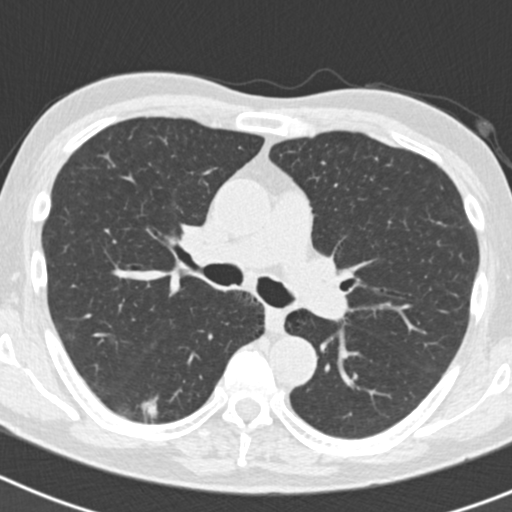
Chest CT (low-dose screening protocol), one axial image; second annual screen; lung window (W 1500 / L -600 HU); standard (soft-tissue) reconstruction kernel (B30f). Male participant, aged 70 years at enrolment.
Expert-annotated lung lesion, bounding box <136,382,193,434> (left, top, right, bottom; pixels). The screening reader recorded 5 non-calcified nodules or masses ≥4 mm on this exam (right lower lobe, right lower lobe, right upper lobe, right upper lobe, left upper lobe); which of them this box marks is not recorded. Official screen result: positive, other. Later outcome: lung cancer diagnosed 622 days after this screen — bronchiolo-alveolar adenocarcinoma, NOS, right lower lobe, poorly differentiated (G3), stage IB (AJCC 6th edition), 30 mm at pathology.